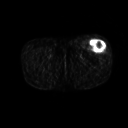
FDG PET of an extremity soft-tissue mass (from a PET/CT study), one axial slice. Slice 228 of 267 in the series (ordered by position). 128 × 128 image matrix. Male patient, age 64 years. From the clinical record (not read from this slice): histological type: extraskeletal osteosarcoma; grade: high; site of the primary tumour: thigh.
Outlined on this slice (expert contour drawn on MRI and transferred to this co-registered scan by the dataset authors):
- gross tumour volume (mass): bounding box [x1, y1, x2, y2] px = [90, 40, 106, 53]